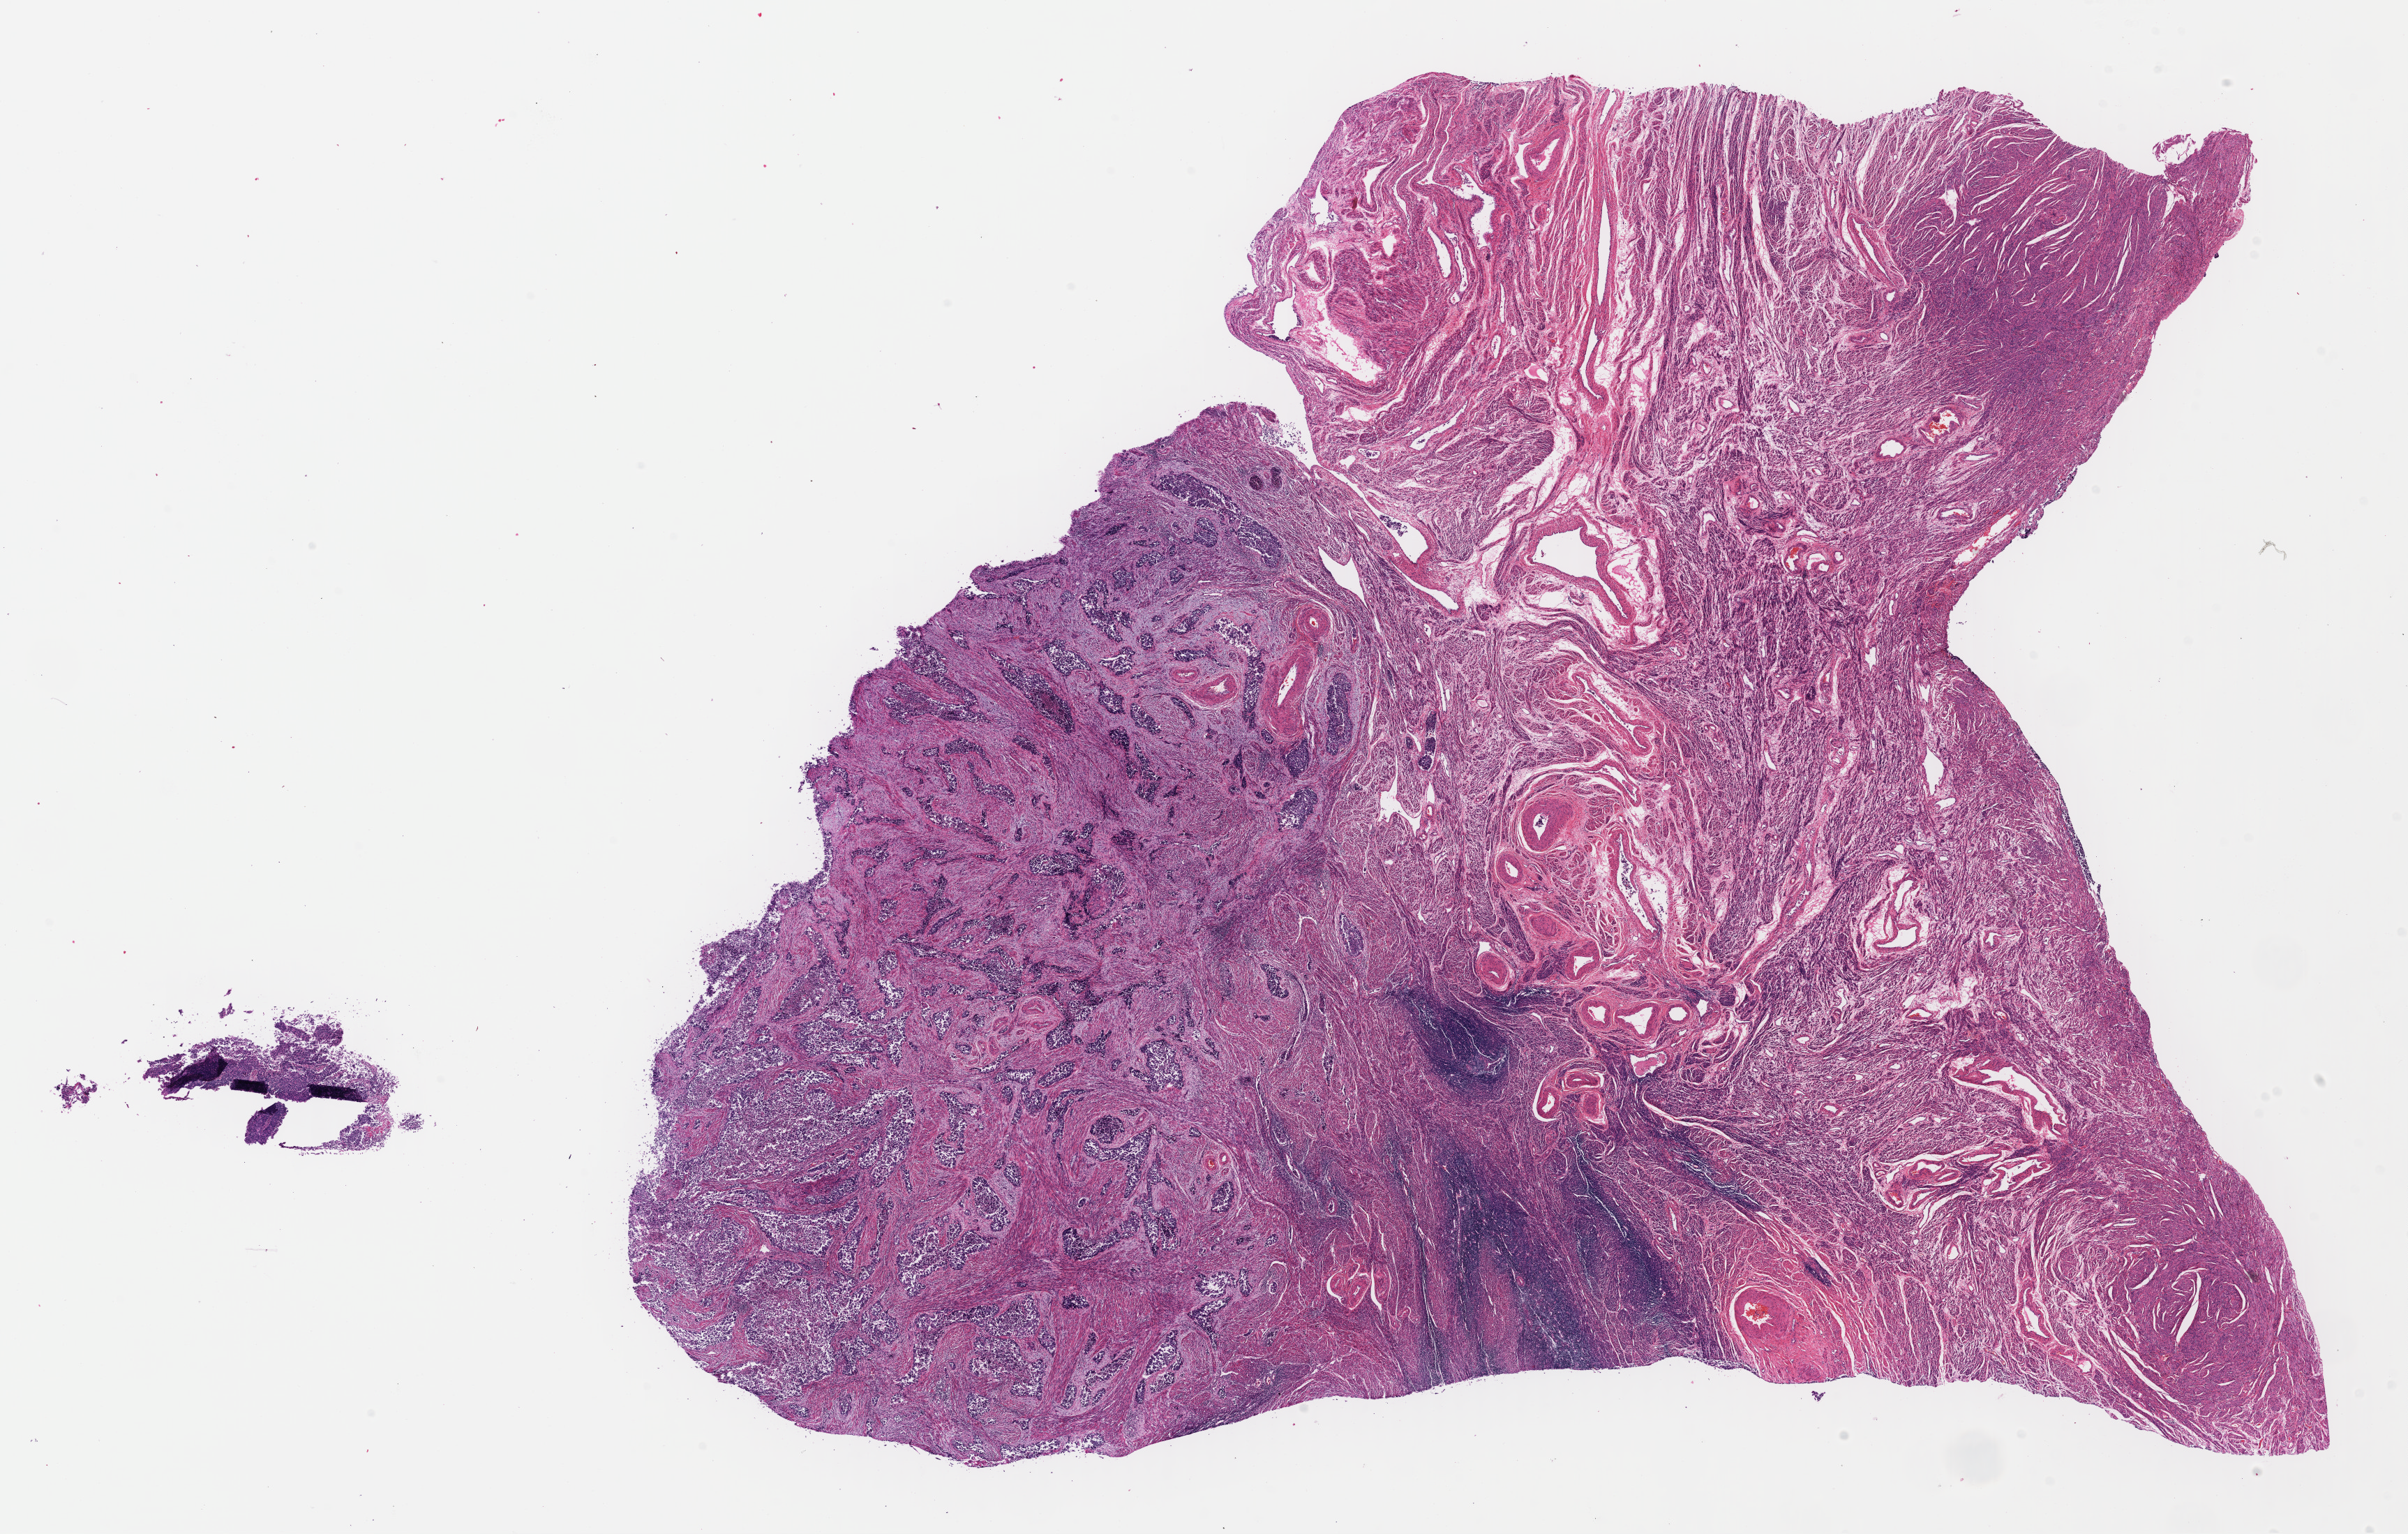
Digitized H&E tissue section (whole slide) — low-resolution overview of the scanned area, about 27.1 x 17.3 mm (from a 40x scan), formalin-fixed paraffin-embedded (FFPE) diagnostic section, uterus, primary tumour sample. Female, age 62 years at initial diagnosis. Histologic grade: G3 (poorly differentiated).
* FIGO stage: IB
* histologic diagnosis: Endometrioid adenocarcinoma, NOS (endometrium)